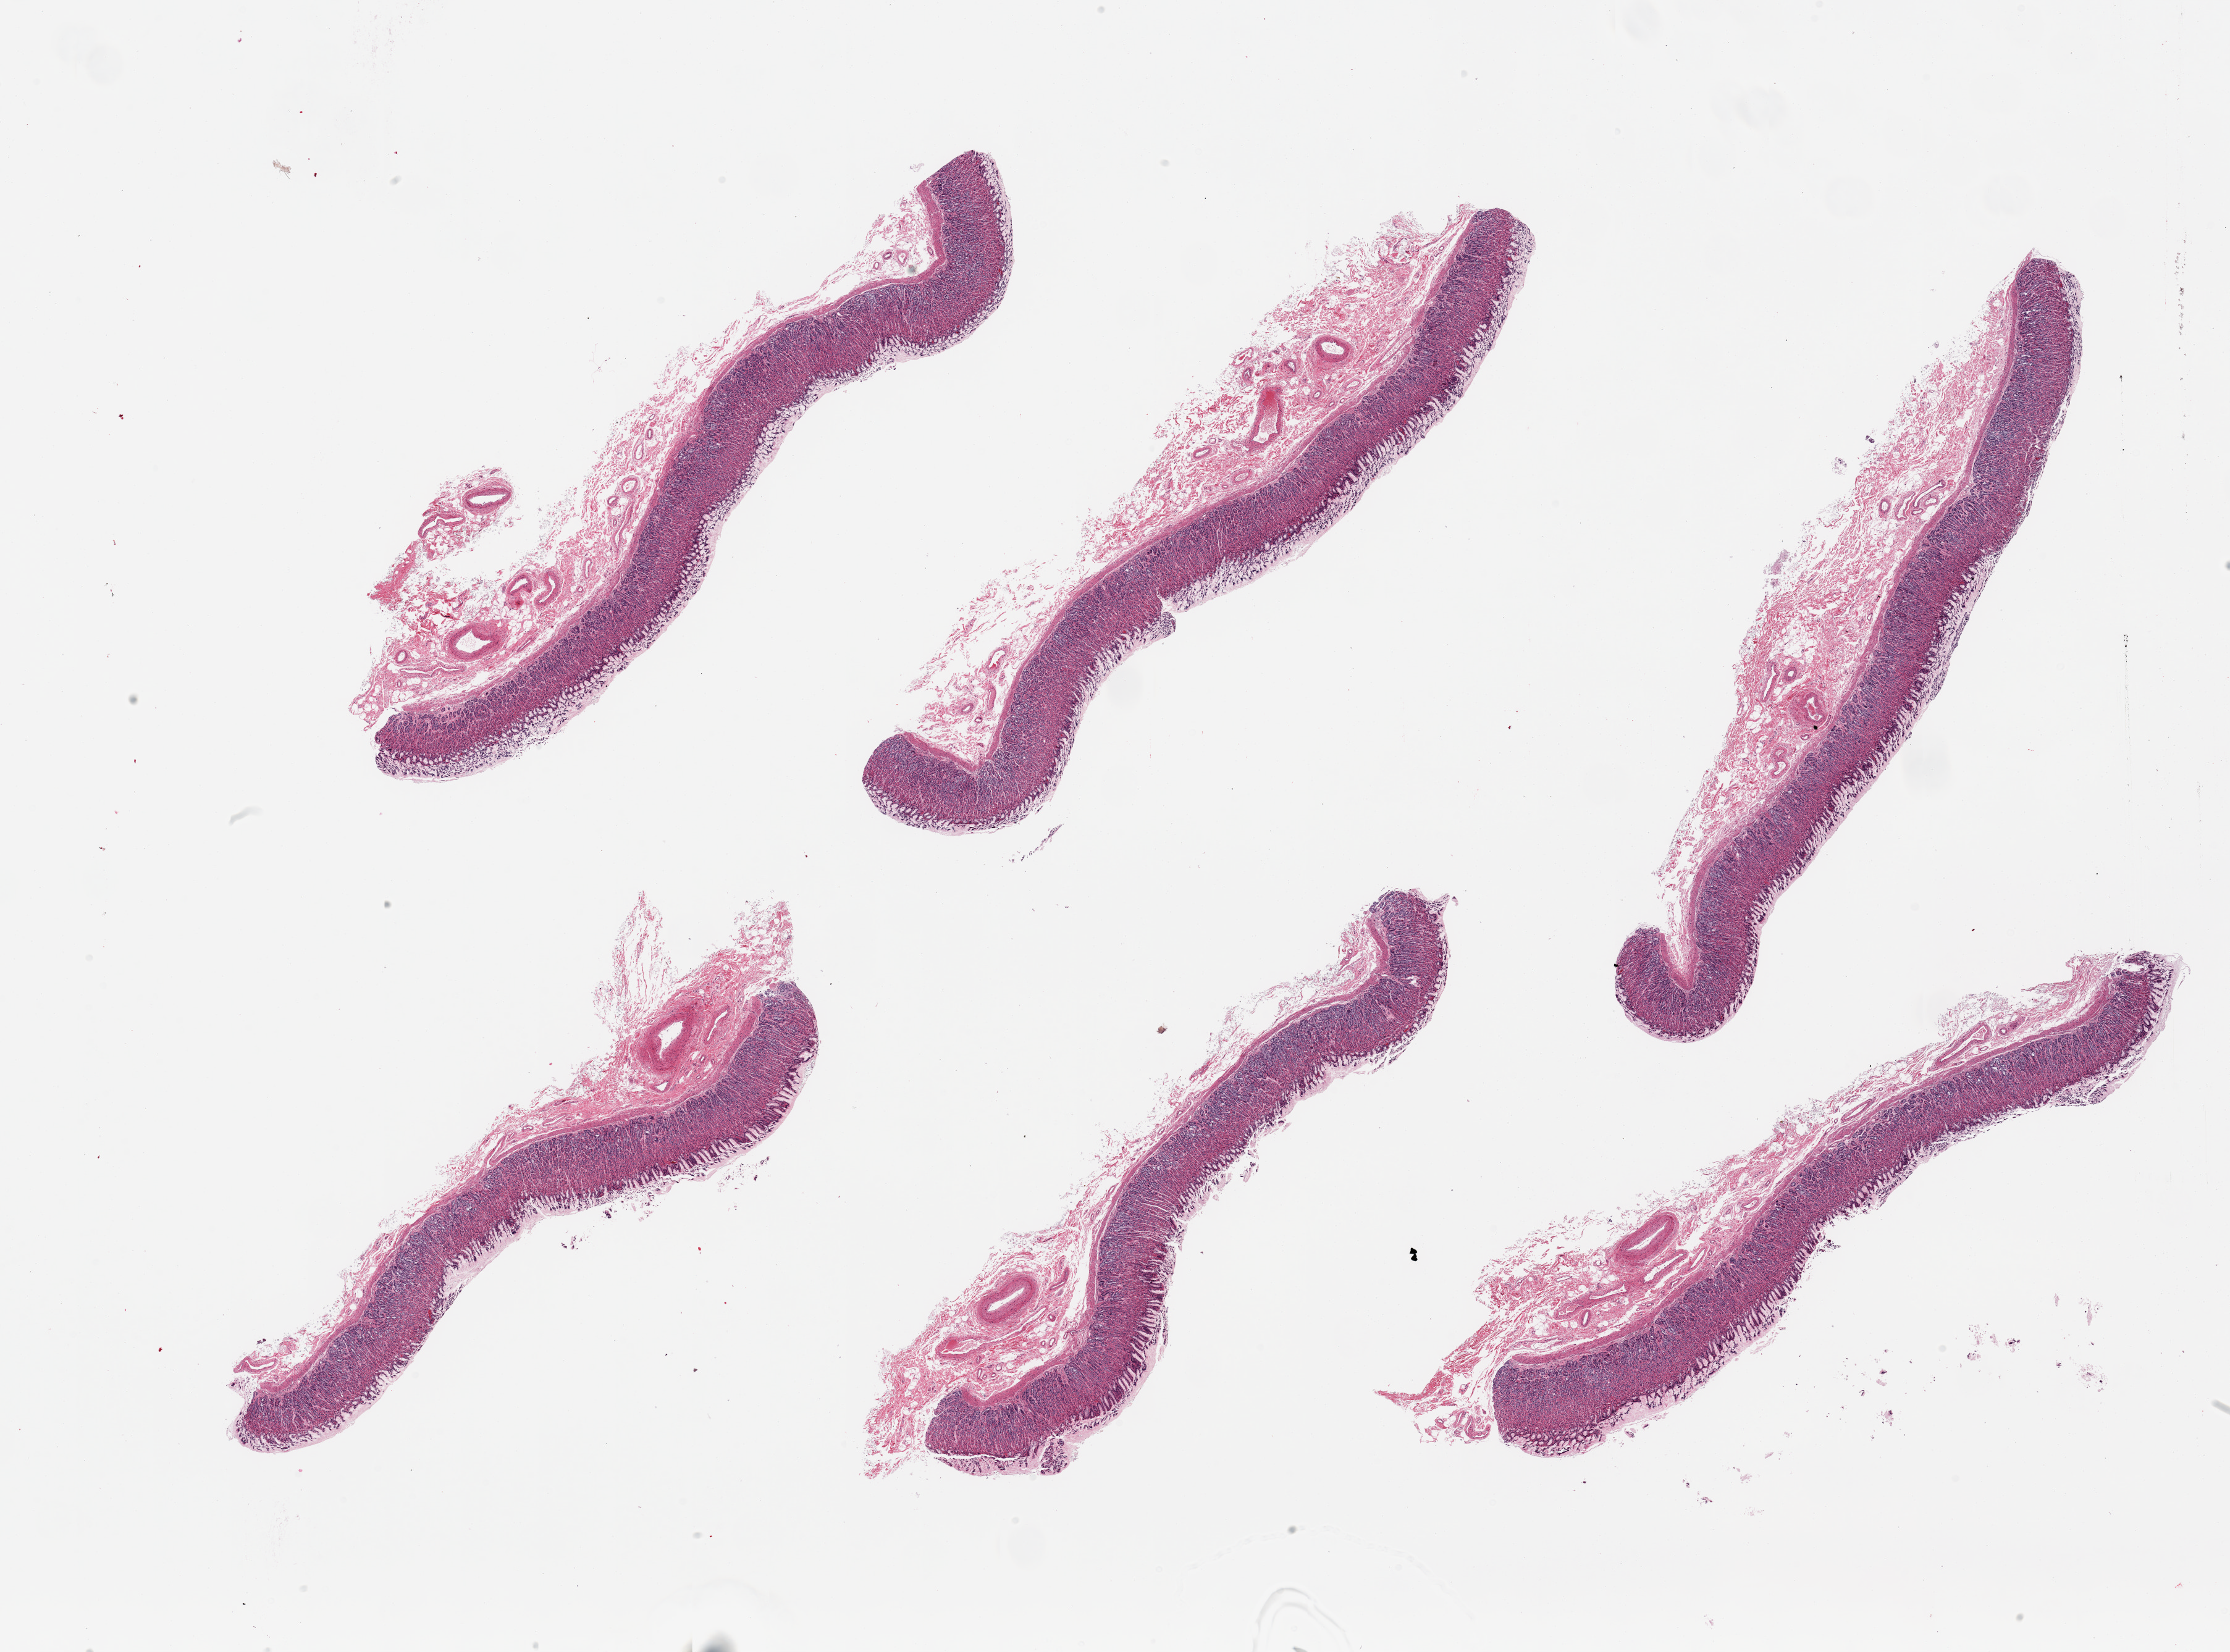
Whole-slide image, haematoxylin and eosin stain, brightfield — whole scanned area (about 28.5 x 21.2 mm) shown as a low-resolution overview. PAXgene-fixed, paraffin-embedded tissue. Section of stomach (target tissue). Donor tissue sample. Male donor.
- review note (as recorded): 6 pieces; essentially well preserved gastric mucosa